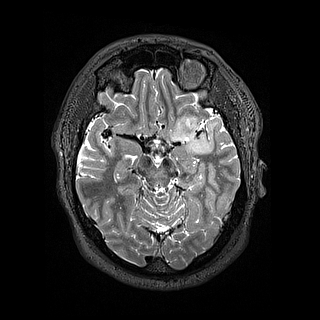
Brain MRI from a brain-tumour surgery series, one axial slice. Slice 97 of 144 in the series (ordered by position). 320 × 320 image matrix. Case-level facts recorded for this patient, not image findings: histopathology: Astrocytoma; WHO grade: 2; IDH mutation: yes; tumour location: Left Insular.
Outlined on this slice (outlined manually by an expert reader):
- tumour: box from (x=171, y=112) to (x=205, y=155) px